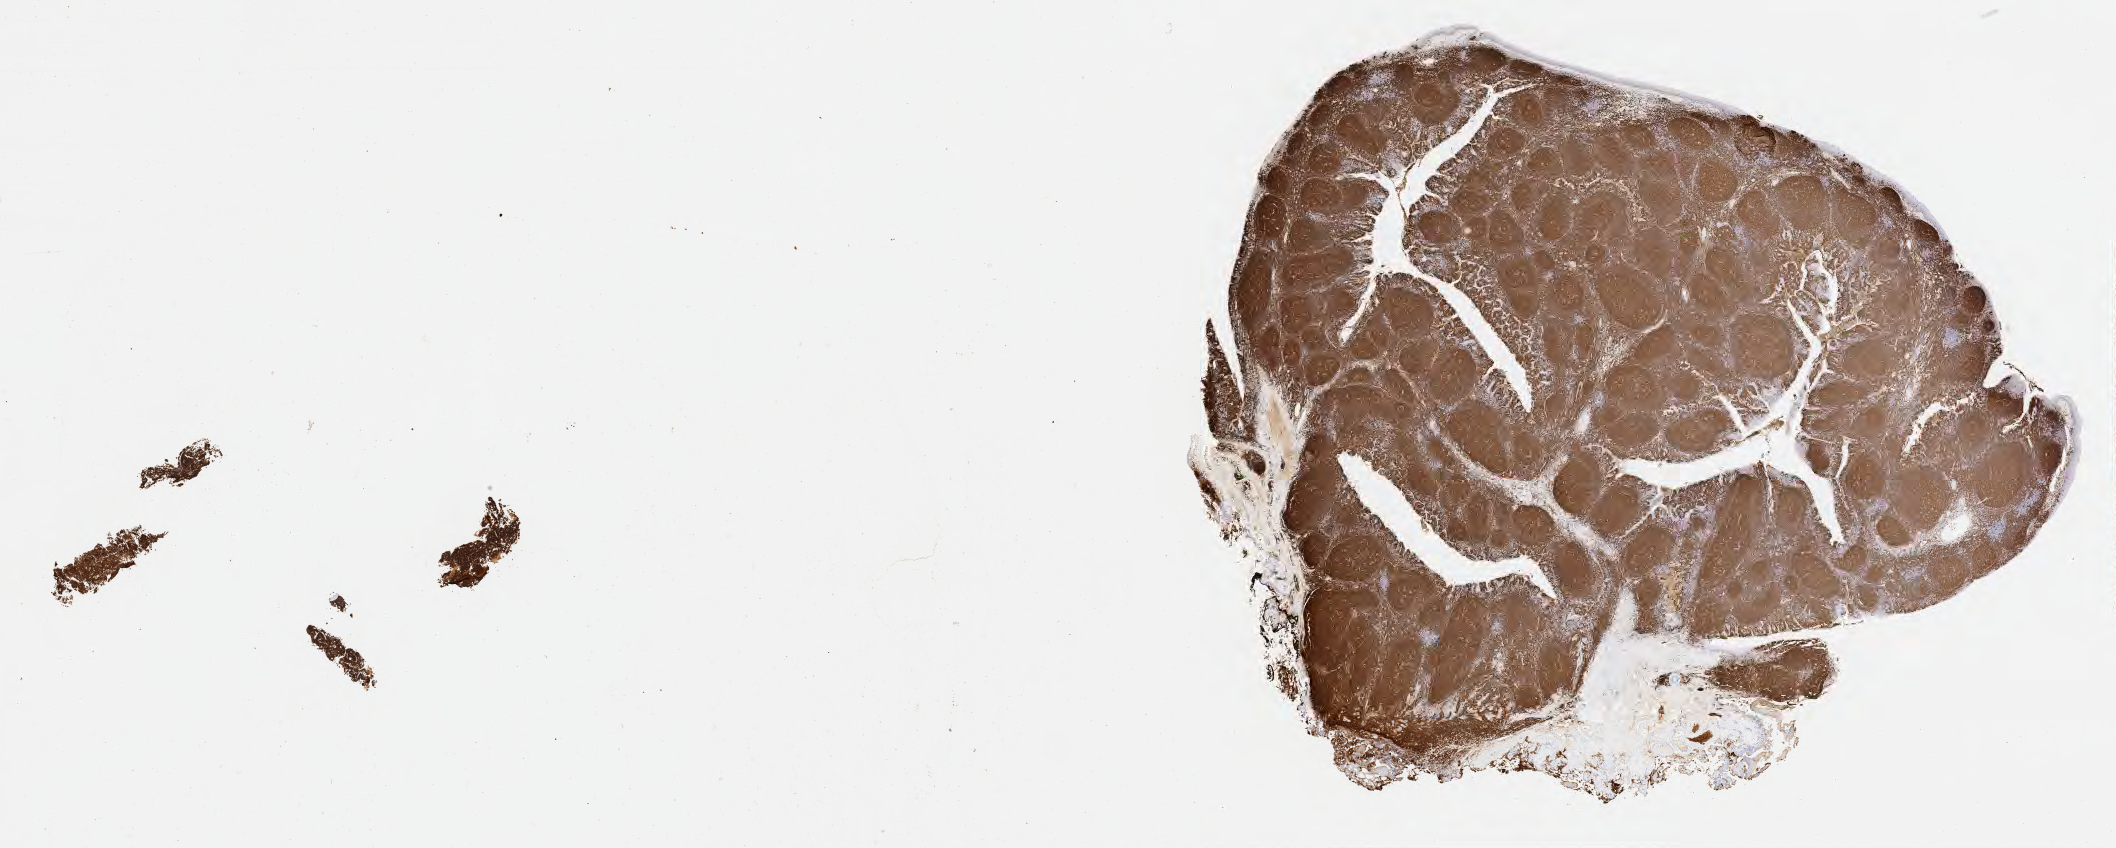
IHC for CD20, whole-slide image — low-resolution overview of the scanned area, about 34.2 x 13.7 mm. Specimen: tumor tissue. Site: lymph node of head and neck. Female patient; age at initial diagnosis 4 years.
Diagnosis: Burkitt lymphoma, NOS.